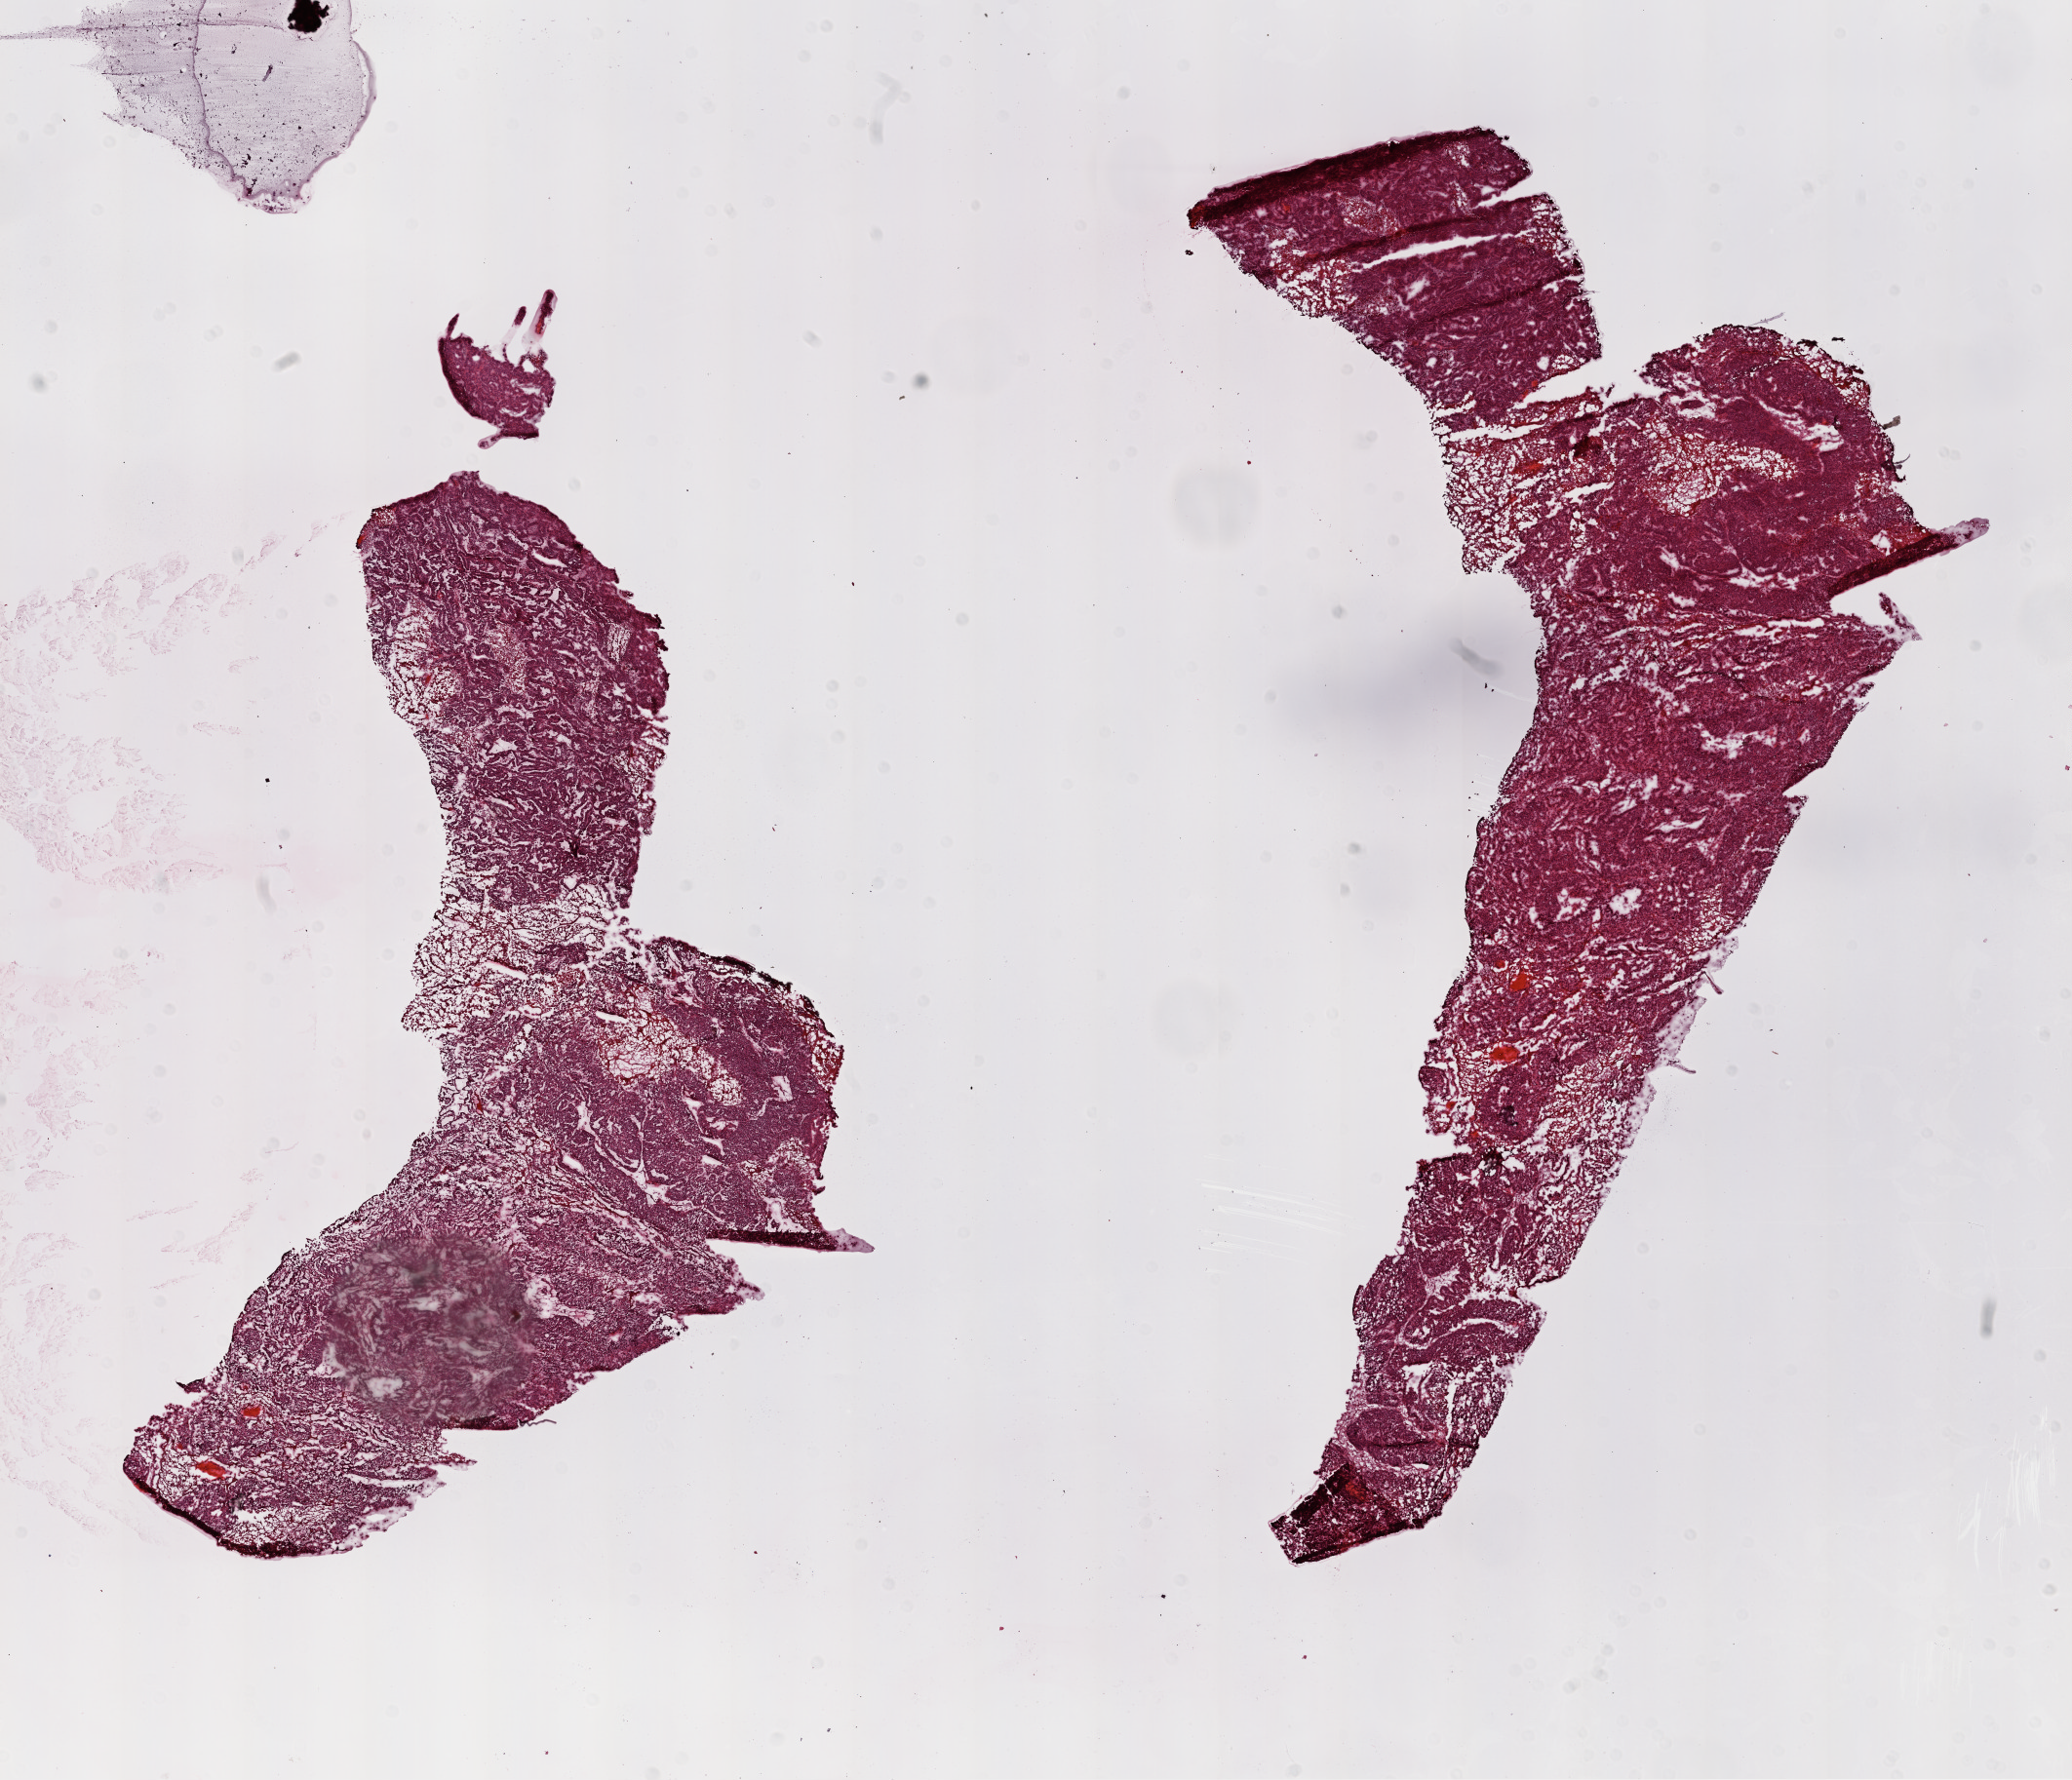
Digitized Hematoxylin and eosin (H&E) stained tissue section (whole slide), whole scanned area (about 17.1 x 14.7 mm, acquisition: 20x scan) shown as a low-resolution overview; frozen section; sample: primary tumour, ovary. Patient: female, age at initial diagnosis 42 years. Histologic grade: G3 (poorly differentiated). Slide review estimates, as recorded: tumour cells 95%, tumour nuclei 95%, normal cells 0%, stromal cells 5%, necrosis 0%. Inflammatory infiltration, as recorded: lymphocyte infiltration 0%, monocyte infiltration 0%, neutrophil infiltration 0%.
Diagnosis: Serous cystadenocarcinoma, NOS. FIGO stage: IIIC. Laterality: bilateral.